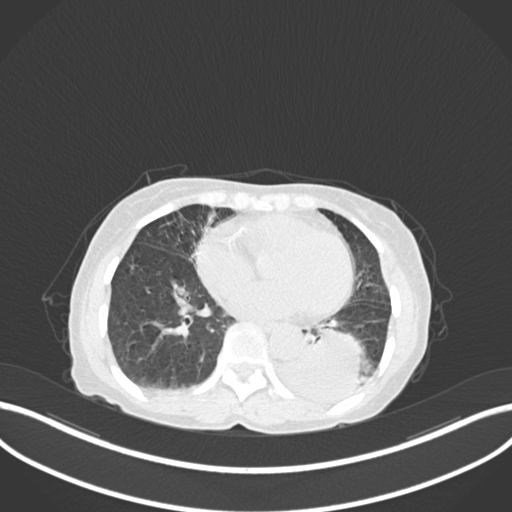
Chest CT, one axial slice; slice 47 of 233 in the series (ordered by position); reconstruction kernel B30f; 120 kVp; lung window (W 1500 / L -600 HU); 1 mm slice thickness; 512 × 512 image matrix, field of view 400 × 400 mm. Female patient, age 78 years. Case-level facts recorded for this patient, not image findings: clinical TNM (as recorded): T3 N0 M1.
Annotated regions visible in this slice (rectangle marked by the reading radiologist):
- lung tumour (recorded histology: squamous cell carcinoma): bounding box <280,322,376,403> (left, top, right, bottom; pixels)